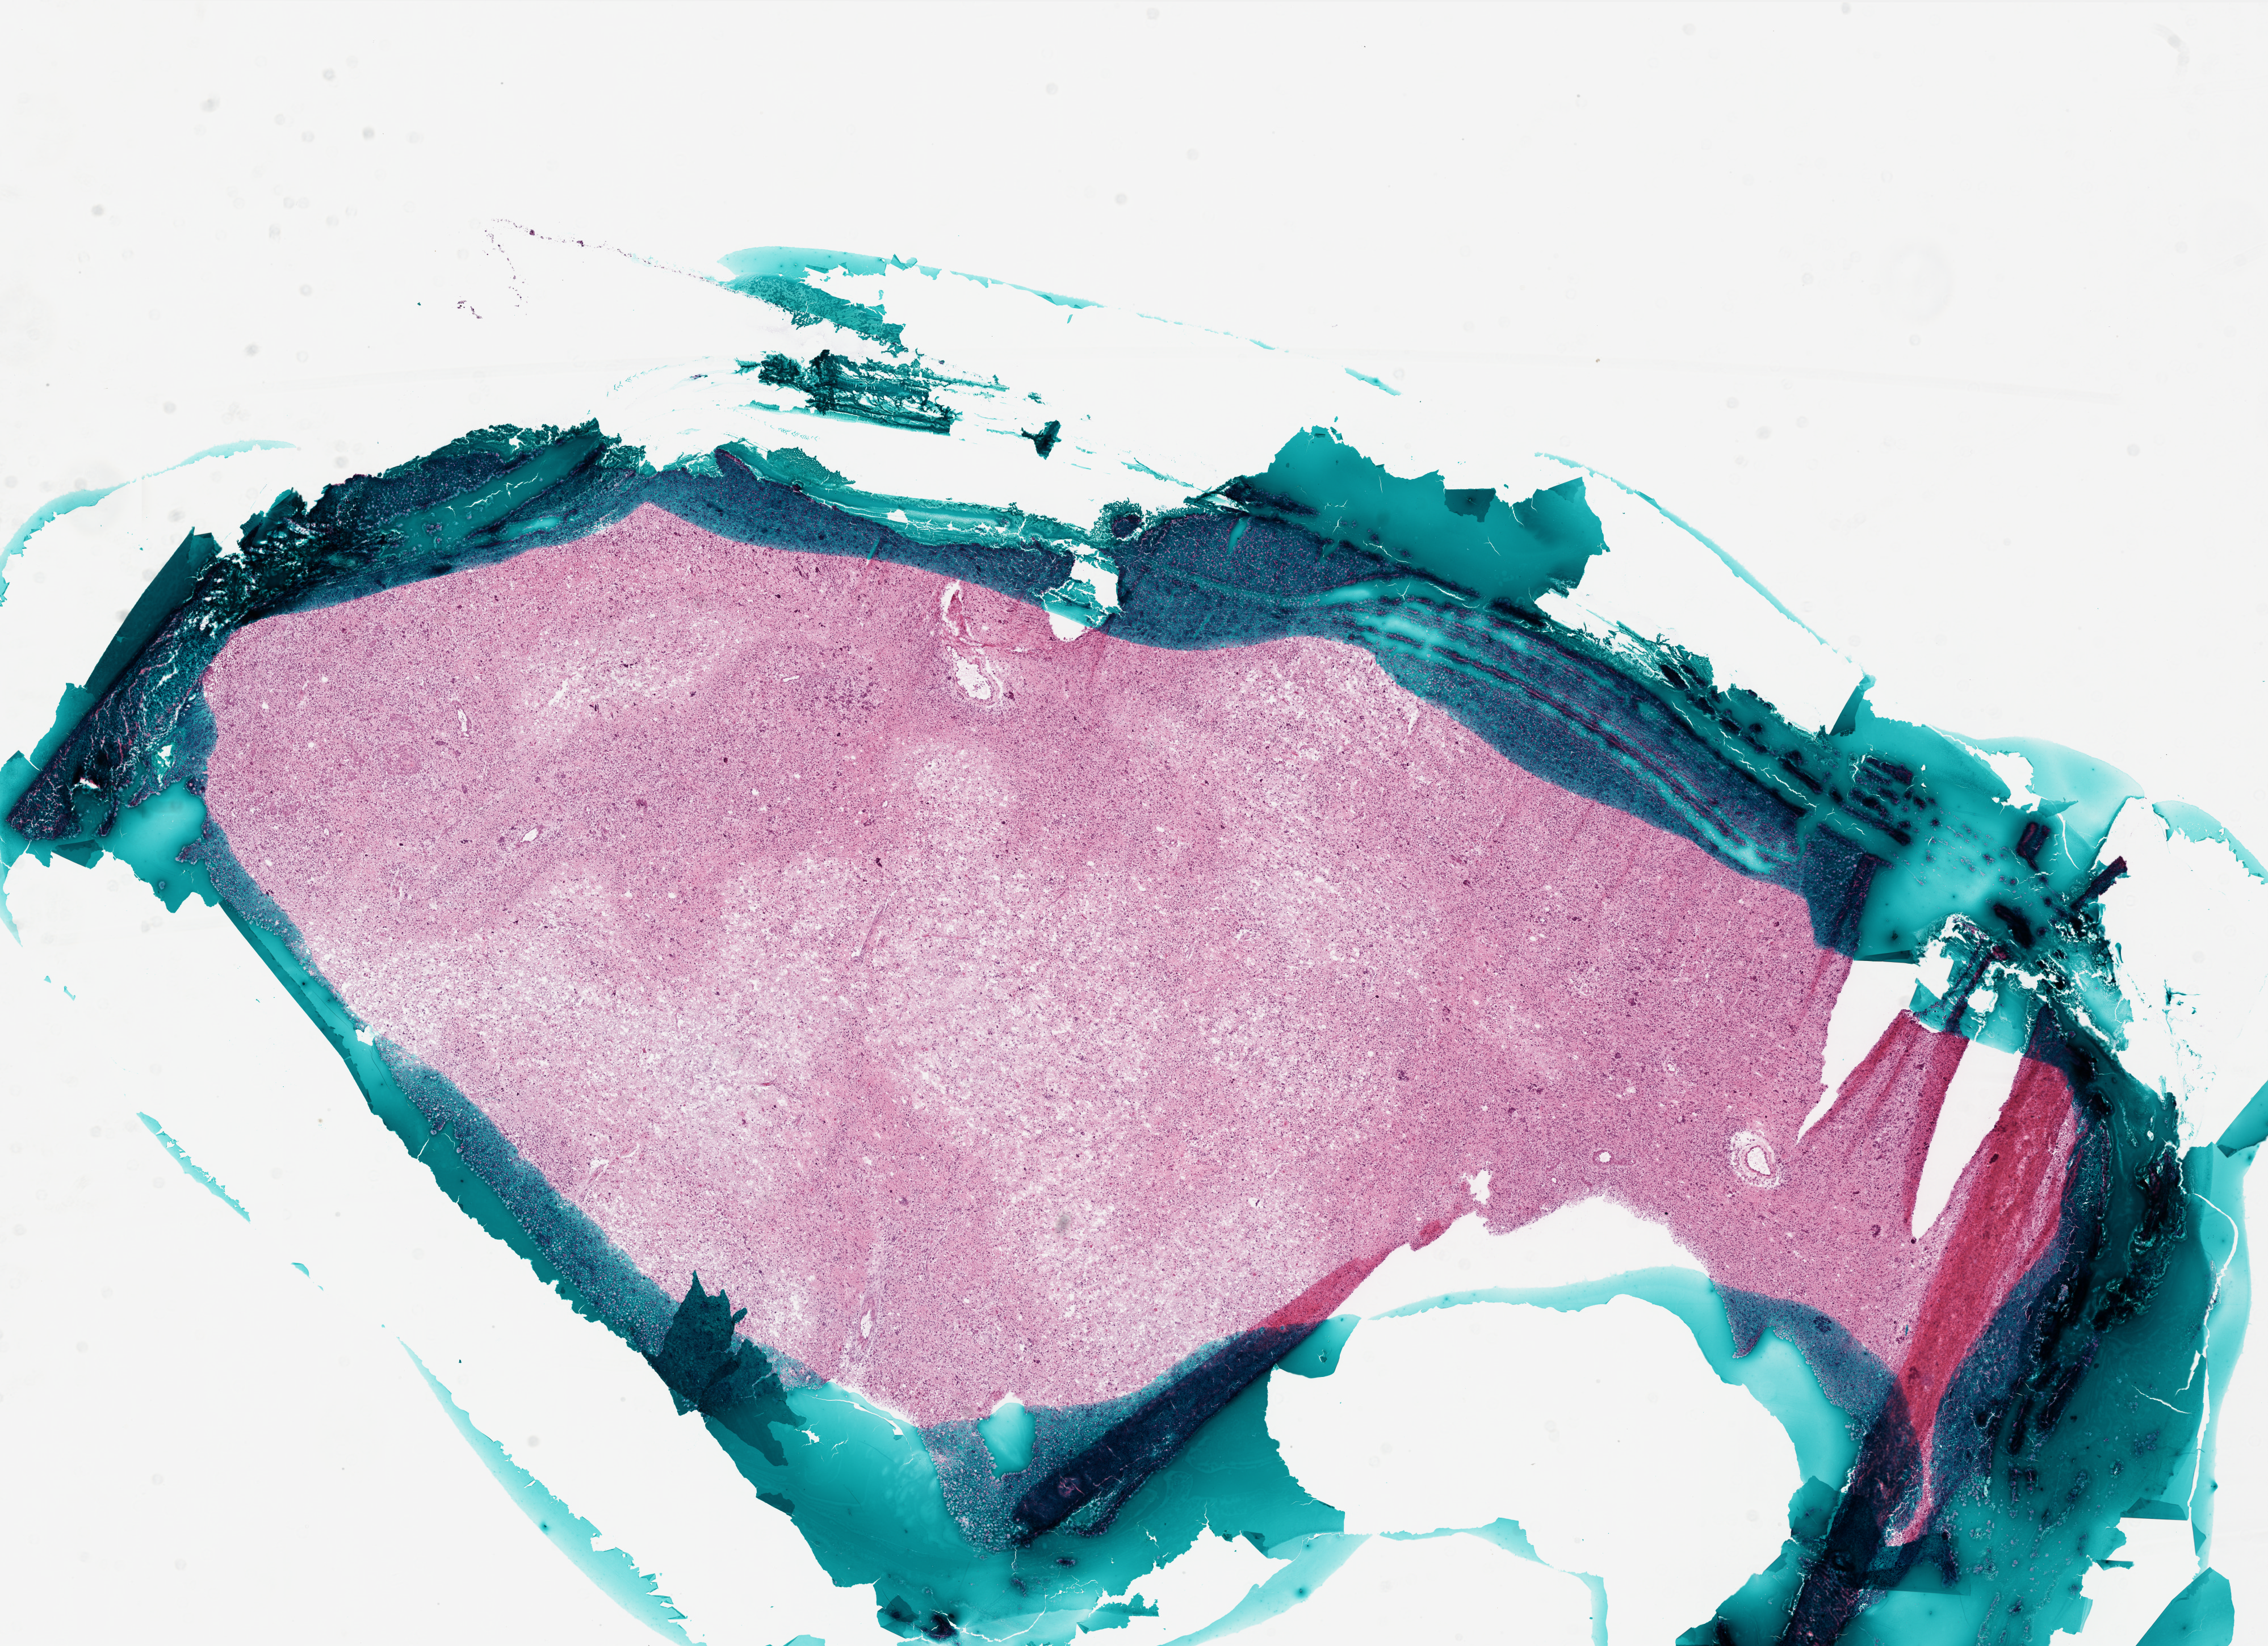
Whole-slide histology image, Hematoxylin and eosin (H&E) stained, a low-resolution overview of the entire scanned area, about 16.0 x 11.6 mm. Frozen section from the bottom of the tissue portion. Brain, primary tumour sample. Male patient; age at initial diagnosis 27 years. Slide review estimates, as recorded: tumour cells 75%, tumour nuclei 100%, normal cells 0%, stromal cells 0%, necrosis 25%.
• diagnosis: Glioblastoma